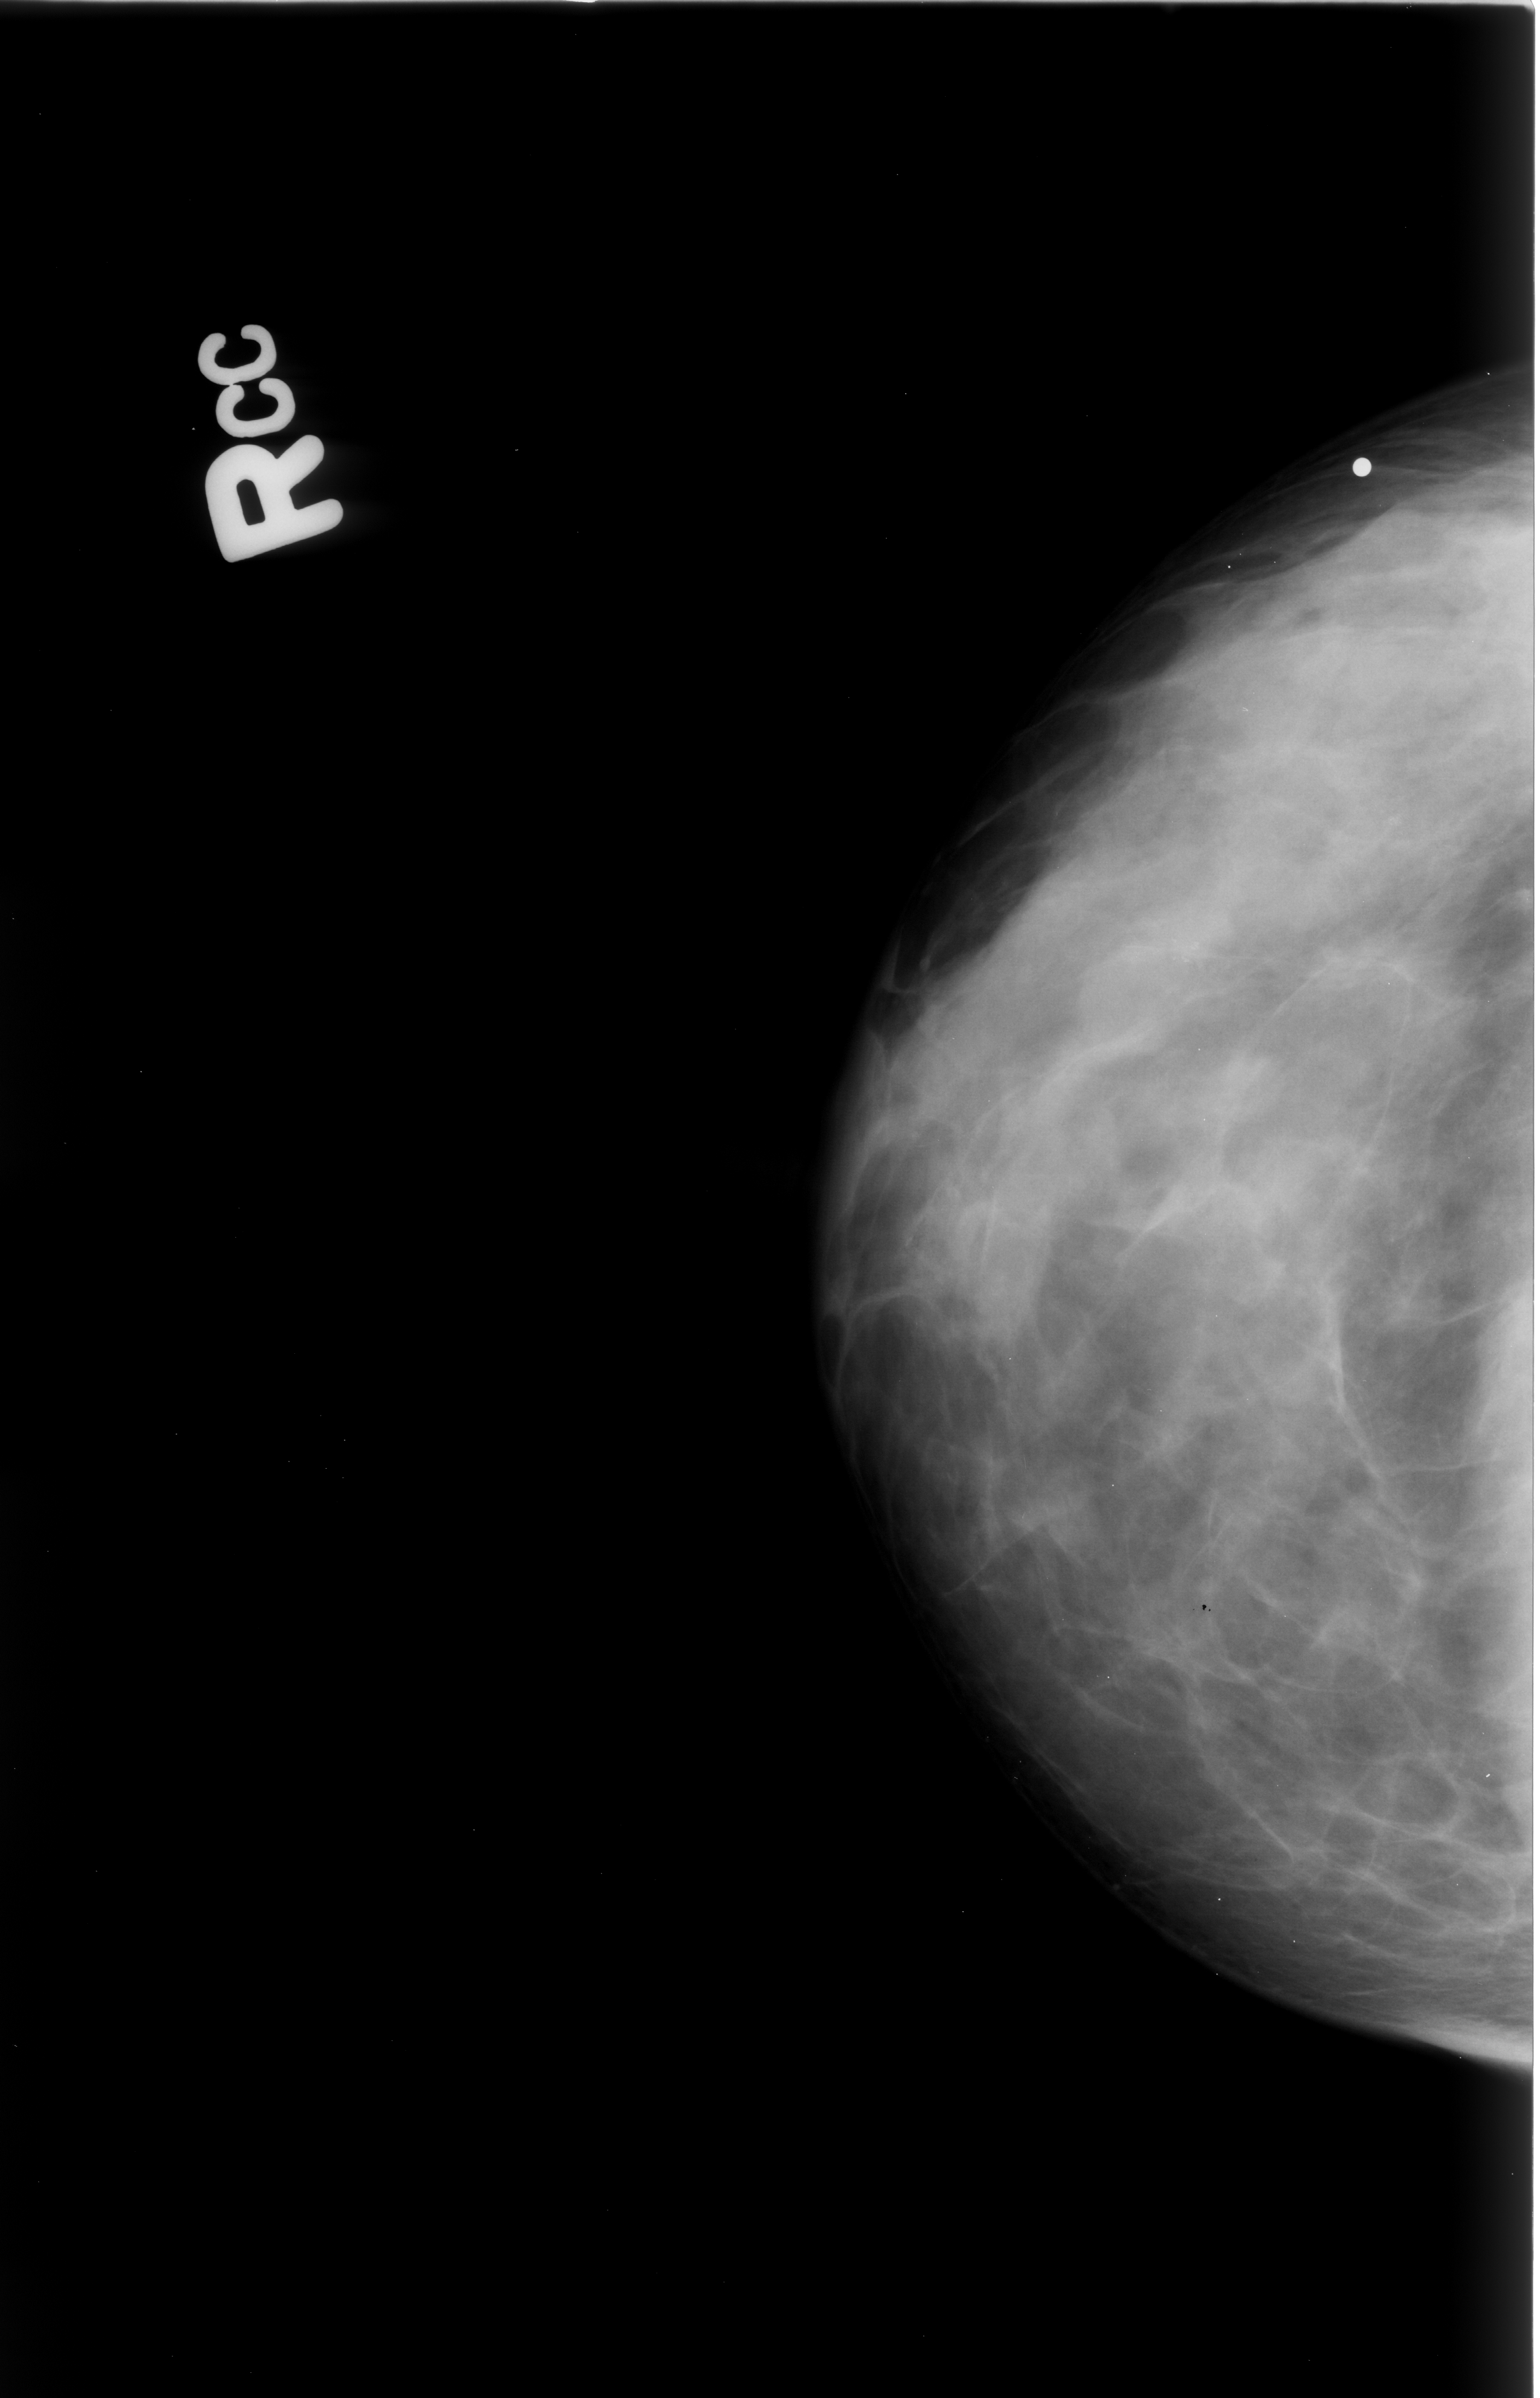
Scanned film-screen mammogram, right breast, CC view, breast composition: heterogeneously dense (BI-RADS density category 3 of 4).
Marked findings (only marked abnormalities are described; nothing is implied about the rest of the image): calcifications, morphology pleomorphic, distribution clustered; BI-RADS assessment category 4; subtlety rating 3 on a 1 (subtle) to 5 (obvious) scale; pathology result (as recorded, not read from the image): benign.